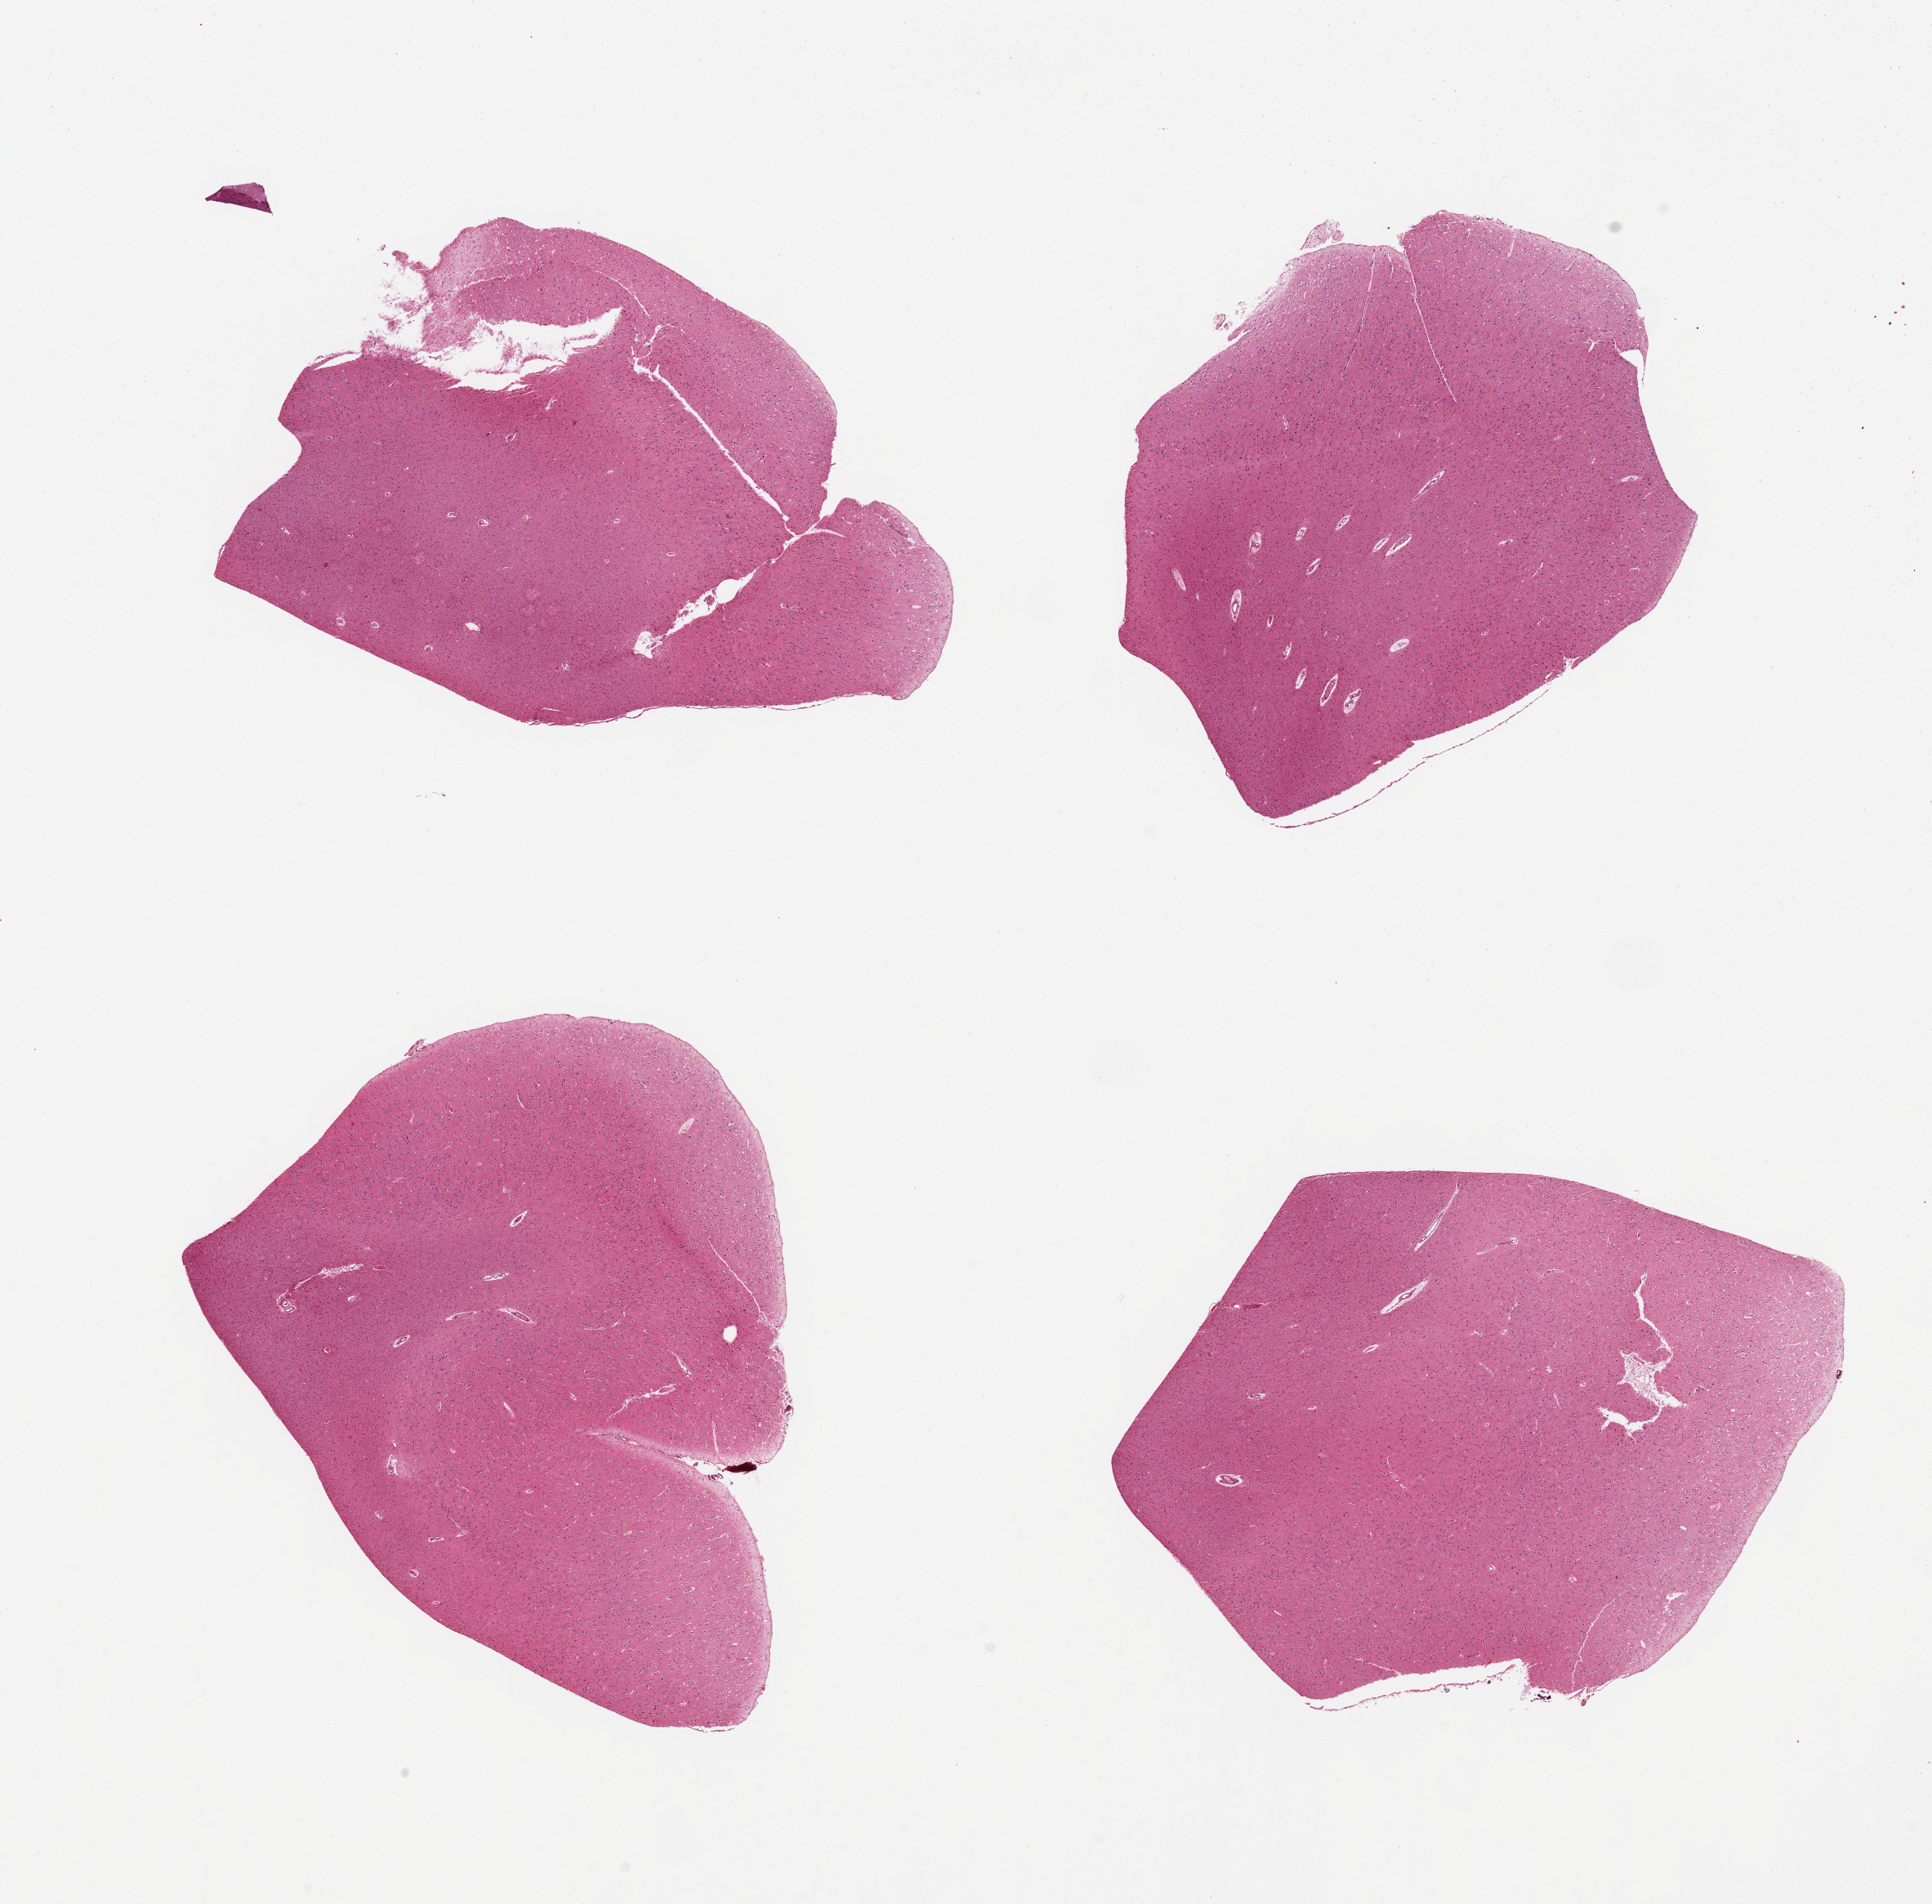
Haematoxylin and eosin whole-slide image, brightfield — shown as a low-resolution overview of the whole scanned area (about 18.7 x 18.4 mm, acquisition: 20x scan). PAXgene-fixed paraffin-embedded (PFPE) section. Section of cerebral cortex (target tissue). Donor tissue sample. Donor sex: female.
Pathologist's review note for this sample: 4 pieces.